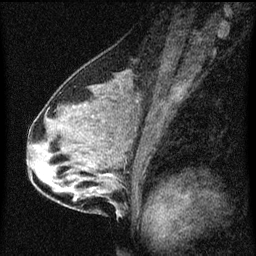
Breast MRI (dynamic contrast-enhanced), one sagittal slice; position 35 of 60 along the scan axis; dynamic contrast-enhanced series, image 2 of 3 at this slice position (ordered by acquisition); 1.5 T; TE 4.2 ms, TR 8 ms; 2 mm slice thickness; 256 × 256 image matrix, field of view 180 × 180 mm. Patient: female, 33 years.
Structures marked on this image (semi-automatic segmentation, software-assisted and operator-edited):
- analysis volume of interest (the breast-tissue region the enhancement analysis was run in; not a lesion): box from (x=61, y=126) to (x=133, y=211) px
- tumour enhancement mask (voxels above the 70 % enhancement threshold inside the analysis volume of interest): (x=107, y=174)–(x=110, y=177)